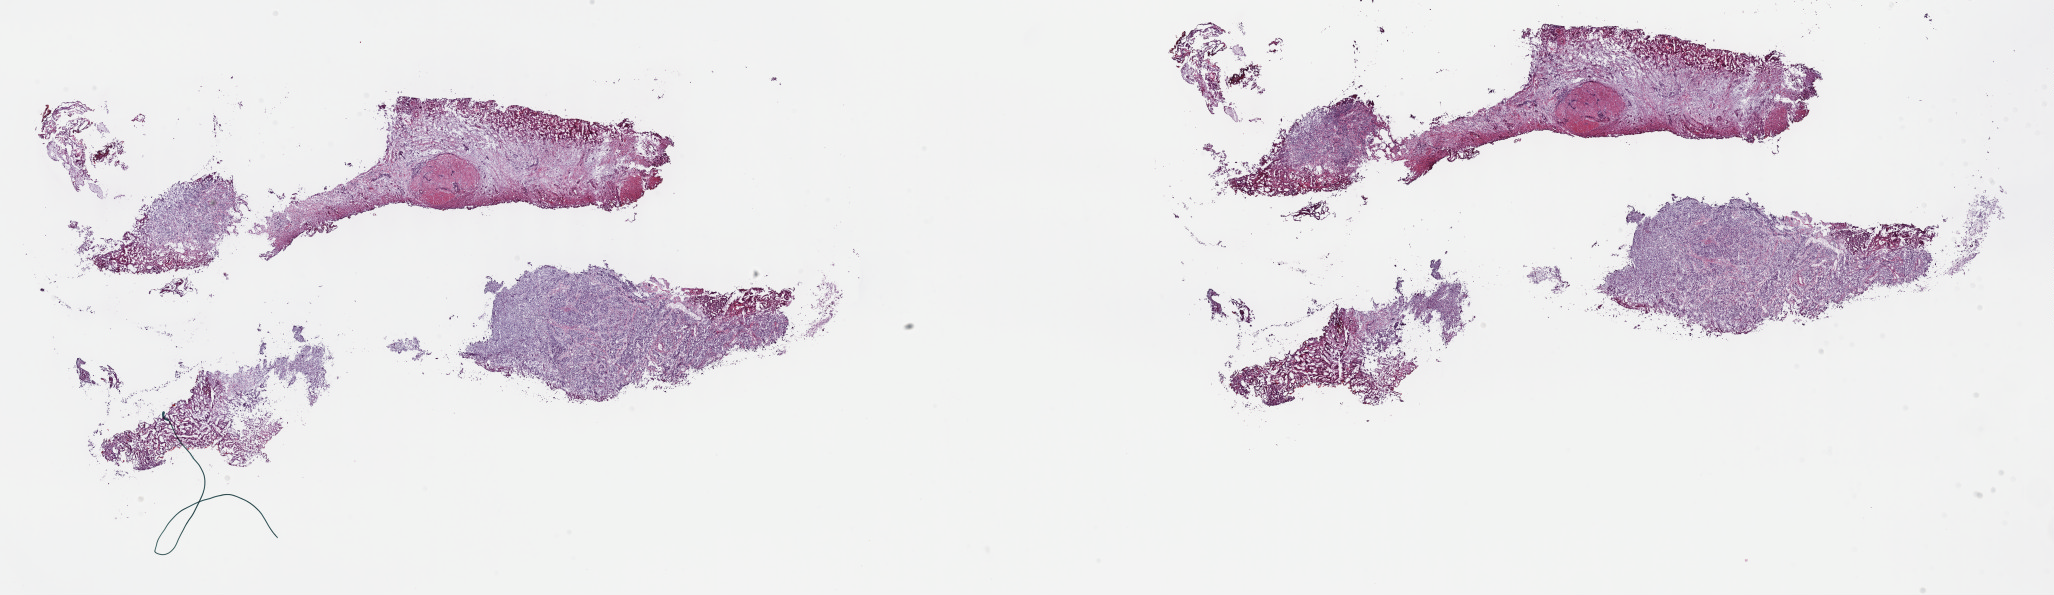
H&E-stained whole-slide image — a low-resolution overview of the entire scanned area, about 33.2 x 9.6 mm. Frozen section from the top of the tissue portion. Sample: primary tumour, bladder. Patient: male, age at initial diagnosis 63 years. Histologic grade: high grade. Slide review estimates, as recorded: tumour cells 100%, tumour nuclei 60%, normal cells 0%, stromal cells 0%, necrosis 0%. Inflammatory infiltration, as recorded: lymphocyte infiltration 4%, monocyte infiltration 0%, neutrophil infiltration 0%.
AJCC pathologic stage: II. Diagnosis: Transitional cell carcinoma (lateral wall of bladder).